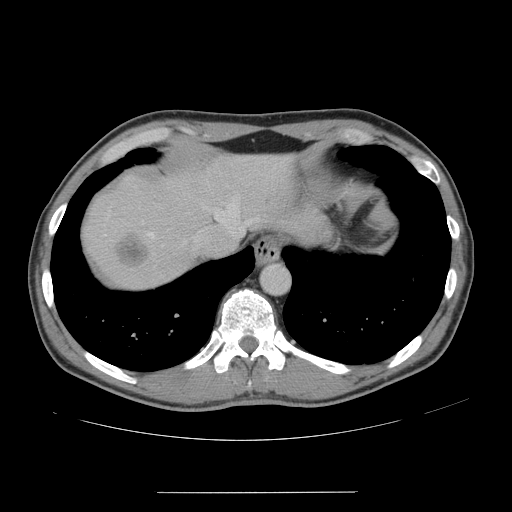
Contrast-enhanced abdominal CT, one axial slice. Position 133 of 178 along the scan axis. Soft-tissue window (W 400 / L 40 HU). 2.5 mm slice thickness. 512 × 512 image matrix. Male patient, age 53 years. Case-level facts recorded for this patient, not image findings: diagnosis: colorectal cancer liver metastases, imaged before liver resection; multiple liver metastases: yes; largest metastasis: 2.4 cm; disease in both lobes: no.
Structures marked on this image (manually delineated by an expert):
- hepatic veins: bounding box [x1, y1, x2, y2] px = [148, 196, 259, 241]
- liver: [84, 156, 292, 288]
- planned liver remnant (the part of the liver to remain after resection): [178, 155, 292, 226]
- liver metastasis: [114, 233, 149, 269]